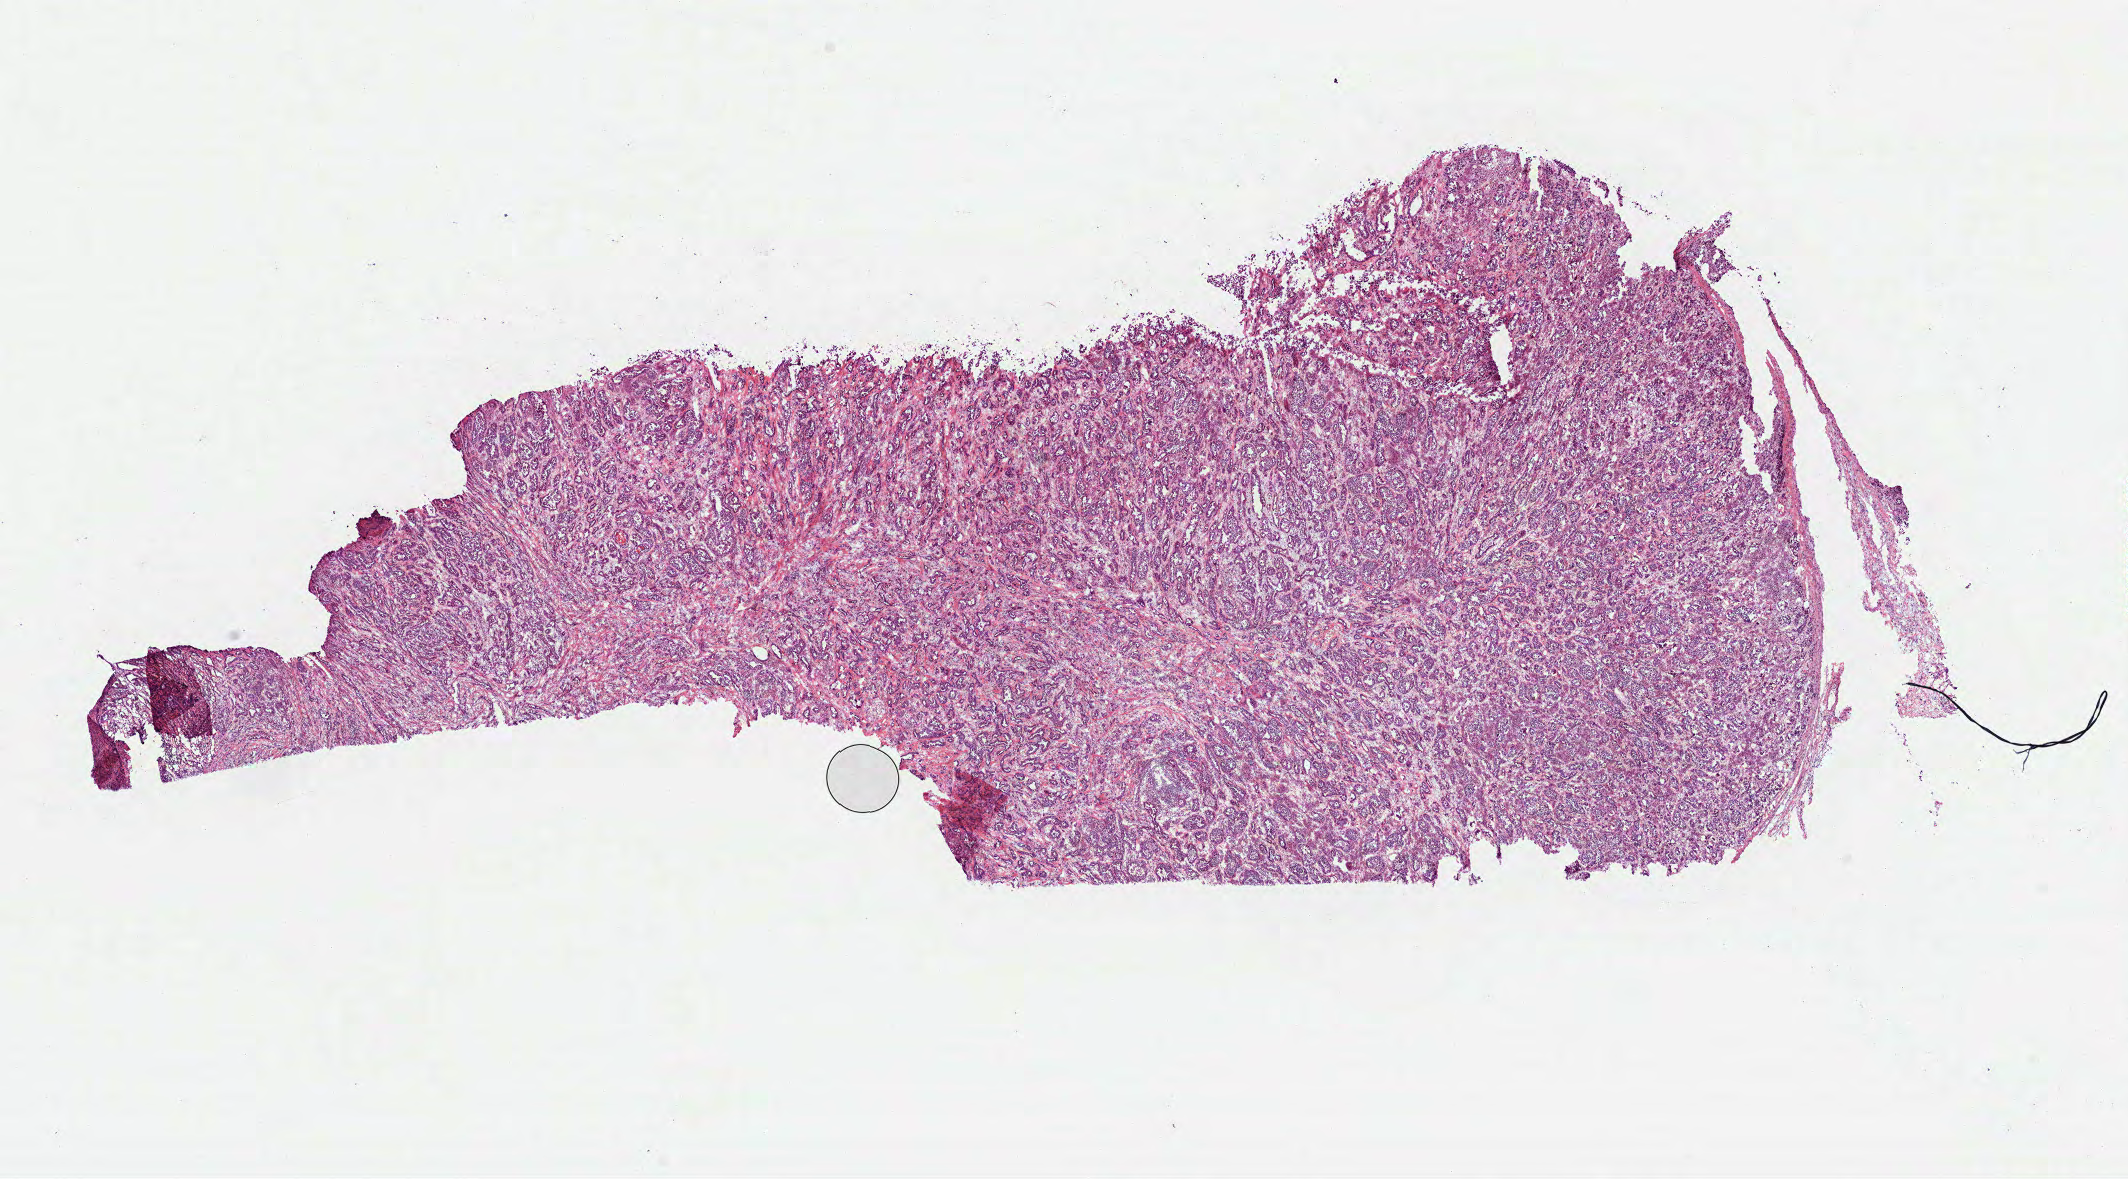
Digitized H&E tissue section (whole slide), whole scanned area (about 17.2 x 9.5 mm, slide scanned at 40x) shown as a low-resolution overview. Frozen section from the bottom of the tissue portion. Lung, recurrent tumour sample. Male patient; age at initial diagnosis 72 years. Slide review estimates, as recorded: tumour cells 100%, tumour nuclei 80%, normal cells 0%, stromal cells 0%, necrosis 0%. Inflammatory infiltration, as recorded: lymphocyte infiltration 5%, monocyte infiltration 5%, neutrophil infiltration 0%.
This section: recurrent tumour. Patient diagnosis: Adenocarcinoma with mixed subtypes (upper lobe, lung).